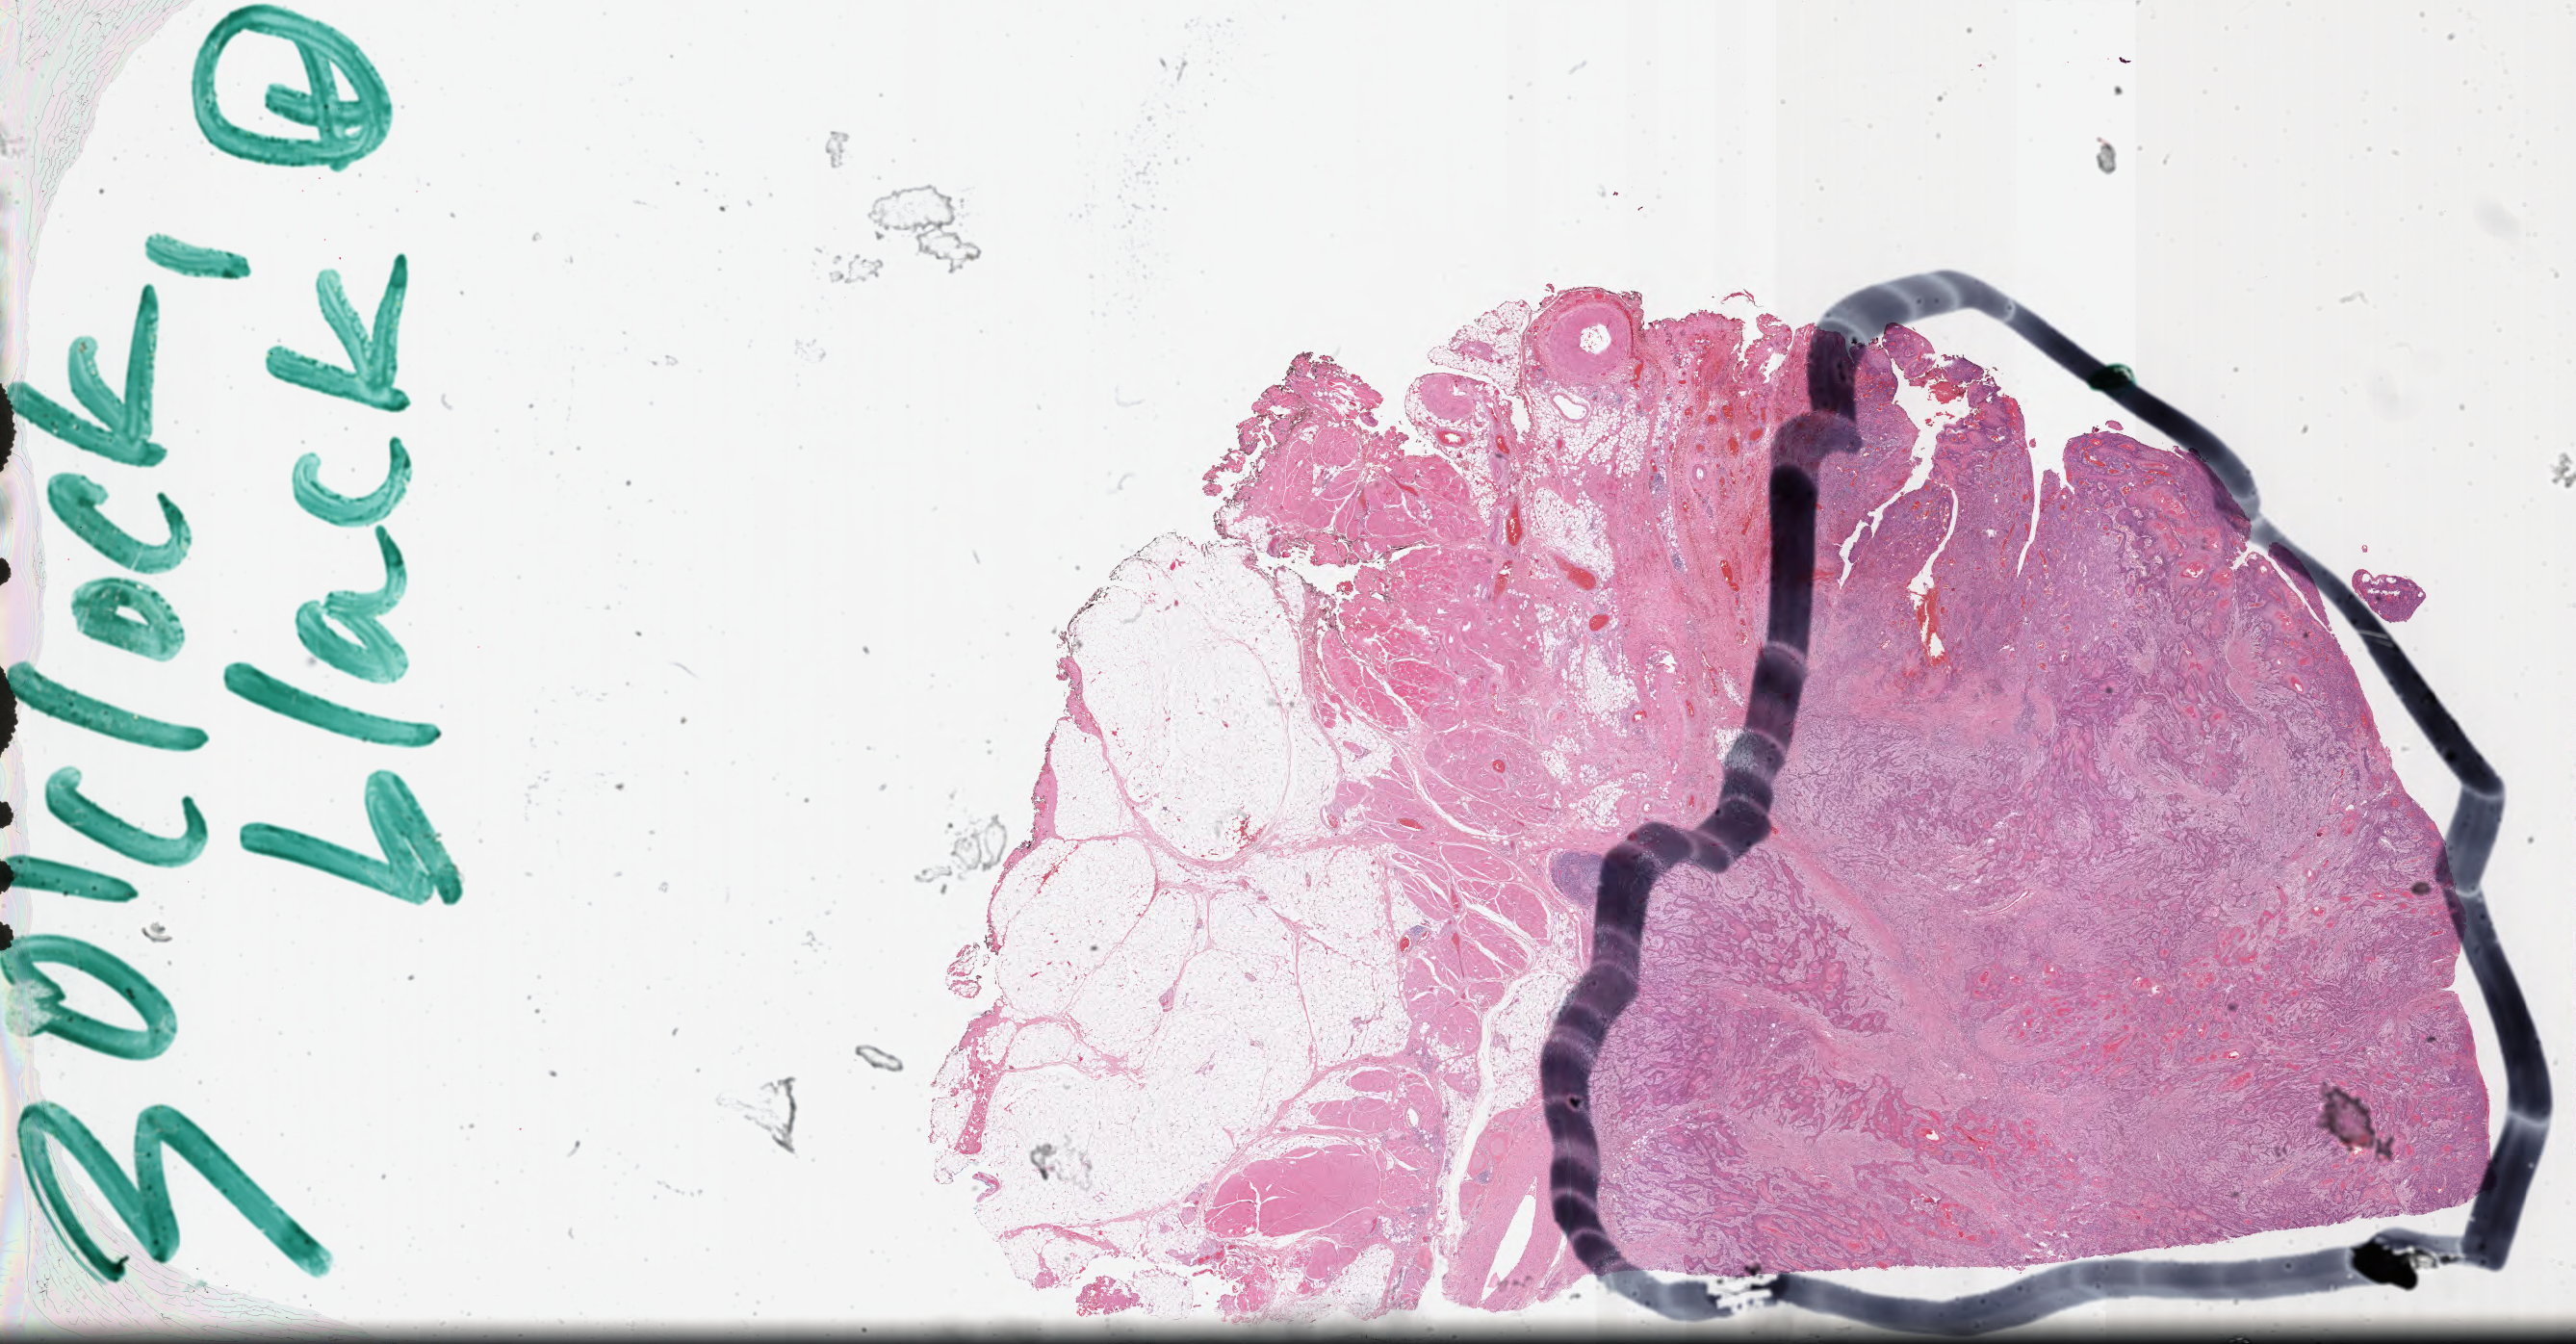
Digitized H&E tissue section (whole slide) — a low-resolution overview of the entire scanned area, about 42.1 x 22.0 mm (acquisition: 40x scan); formalin-fixed paraffin-embedded (FFPE) diagnostic section; sample: primary tumour, head and neck. Male, age 45 years at initial diagnosis. Histologic grade: G2 (moderately differentiated).
AJCC pathologic stage: IVA (6th edition). Pathologic diagnosis: Squamous cell carcinoma, NOS (cheek mucosa). Laterality: left.